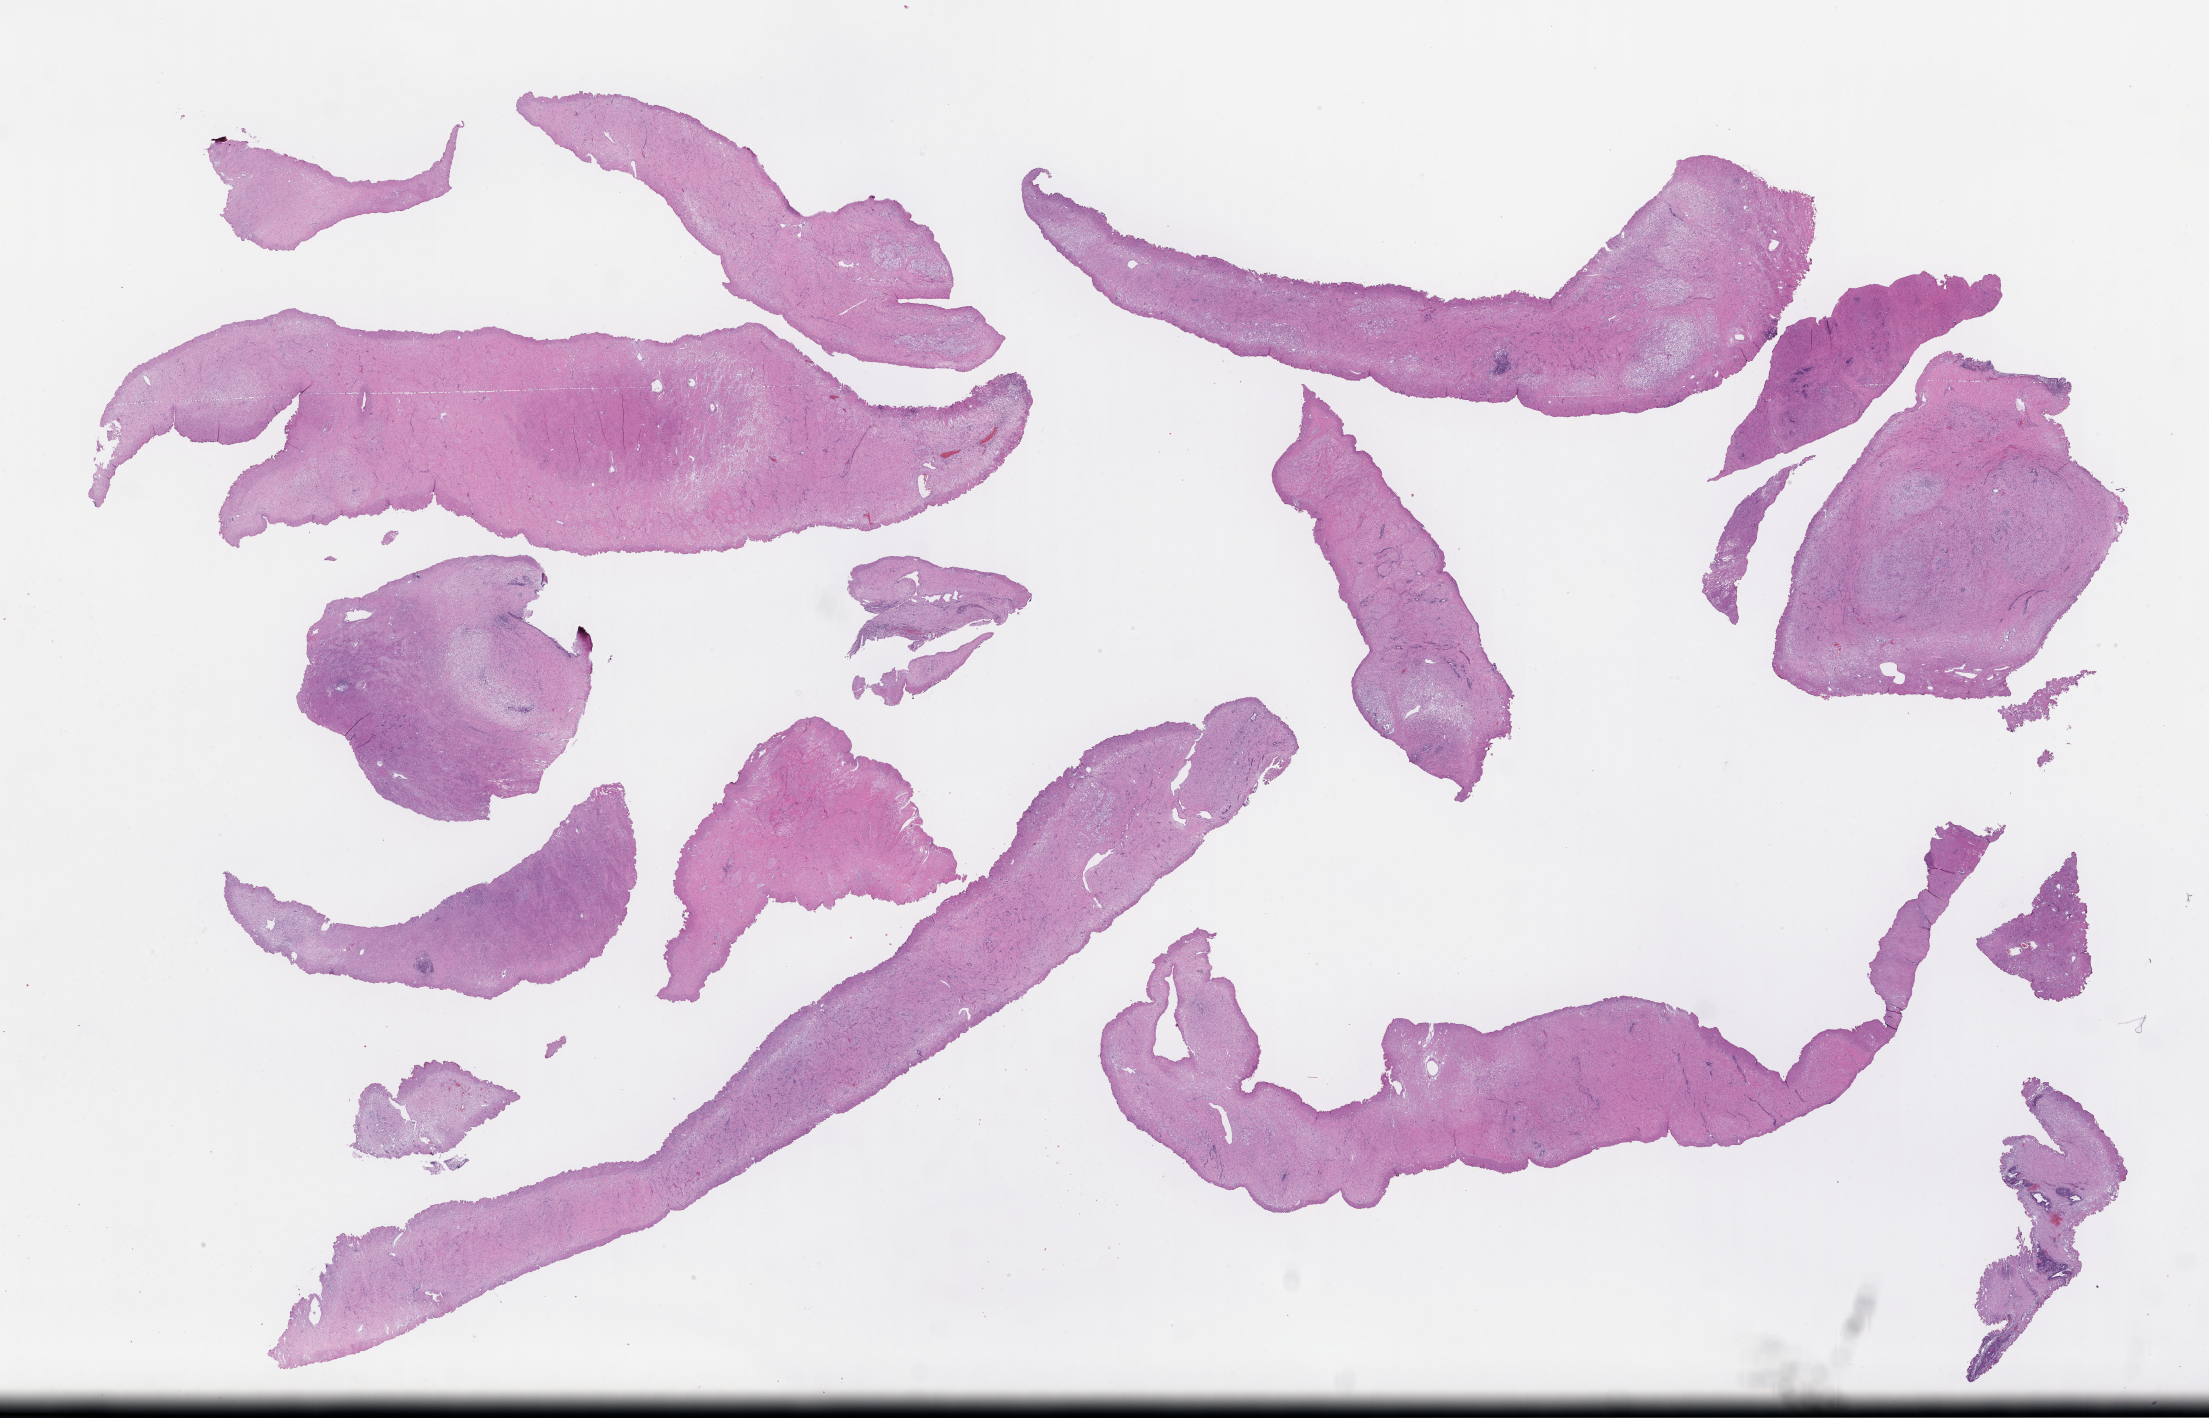
Whole-slide image, hematoxylin and eosin (H&E) stain — whole scanned area (about 35.7 x 22.9 mm) shown as a low-resolution overview; formalin-fixed paraffin-embedded section; site: prostate. Patient: male.
This section: primary tumor. Diagnosis: Prostate Carcinoma.